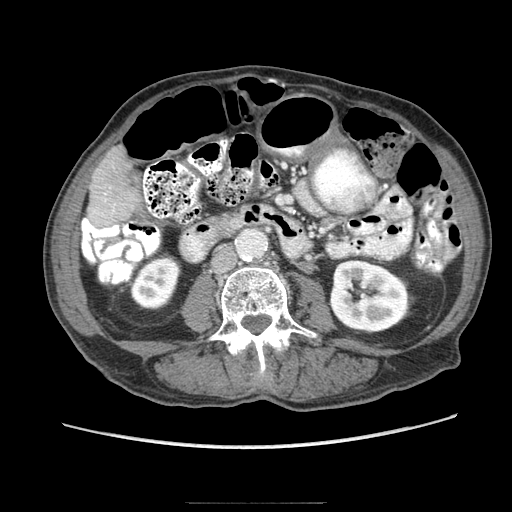
Contrast-enhanced abdominal CT (liver protocol), one axial slice; reconstruction kernel STANDARD; 140 kVp; soft-tissue window (W 400 / L 40 HU); 512 × 512 image matrix, field of view 360 × 360 mm. From the clinical record (not read from this slice): diagnosis: hepatocellular carcinoma (patient treated with transarterial chemoembolisation; whether this scan precedes or follows treatment is not stated here); TNM stage (as recorded): Stage-I.
Outlined on this slice (semi-automatic segmentation, software-assisted and operator-edited):
- liver parenchyma outside the tumour (the mass and vessels are separate outlines, so this box may not span the whole liver): bounding box (x1, y1, x2, y2) in pixels: (87, 146, 140, 228)
- liver vessels: (89, 199, 116, 224)